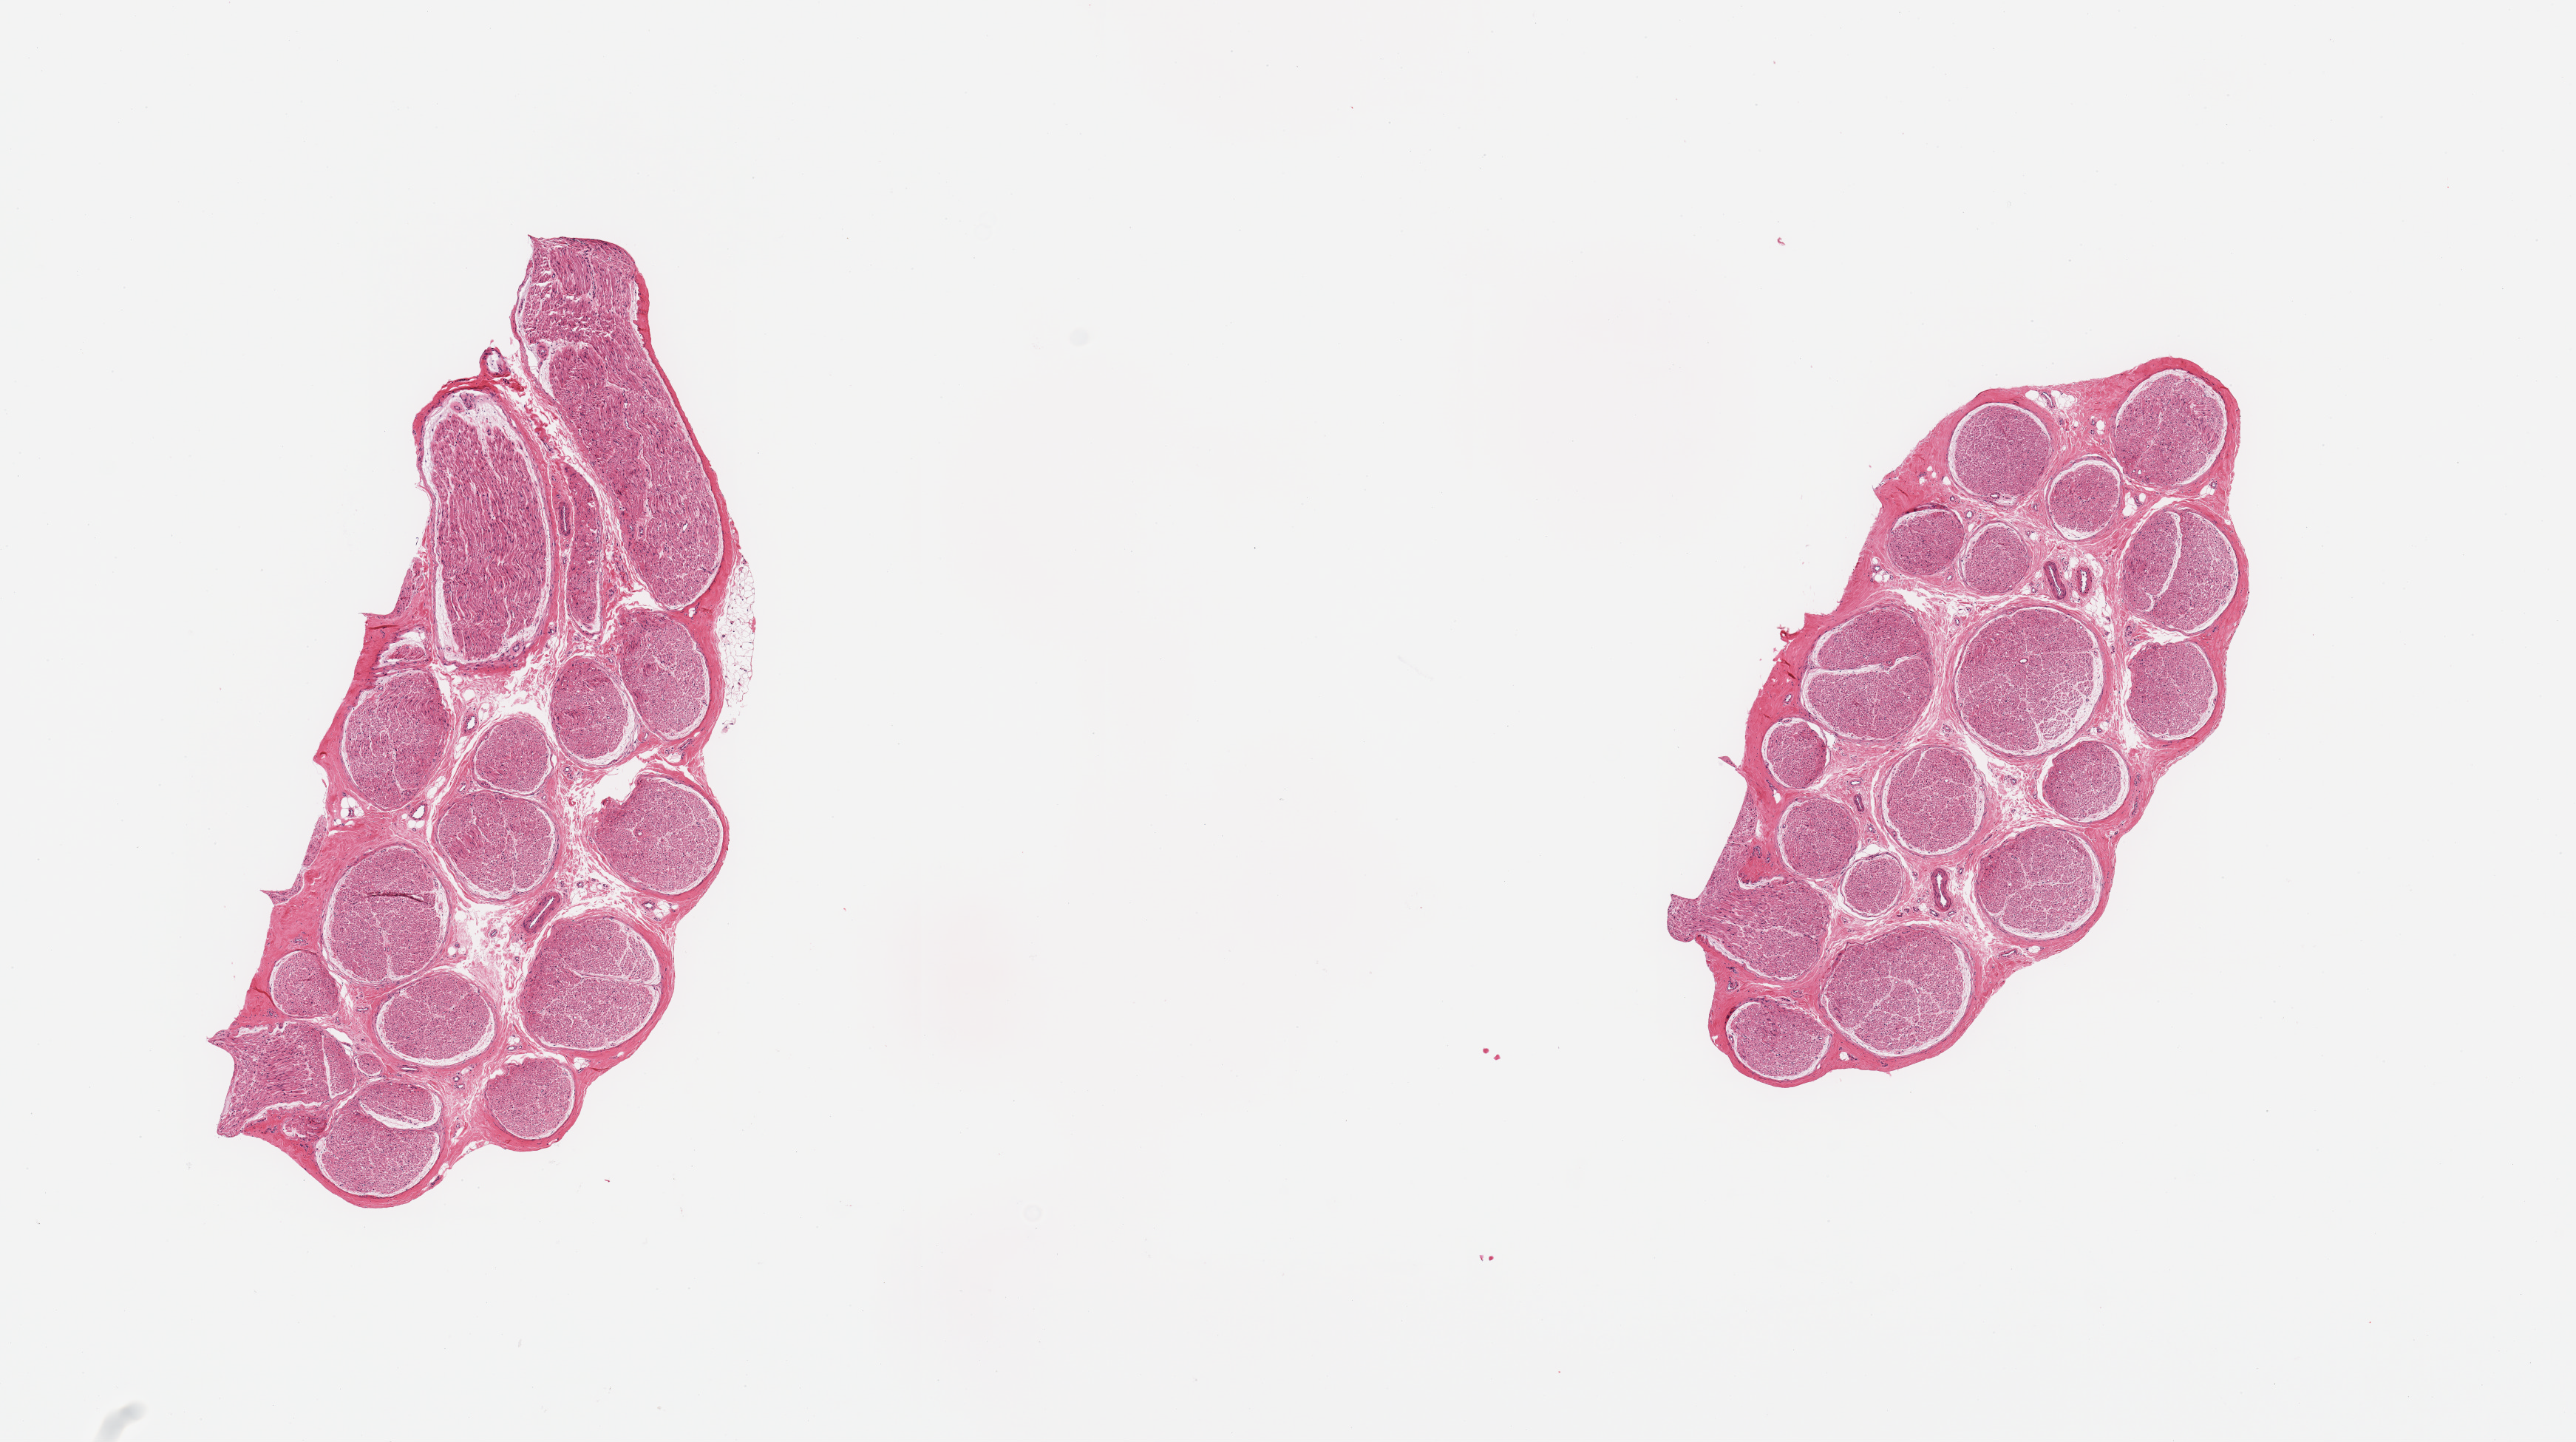
Haematoxylin and eosin whole-slide image, brightfield, low-resolution overview of the scanned area, about 13.8 x 7.7 mm. PAXgene-fixed paraffin-embedded (PFPE) section. Target tissue: tibial nerve. Tissue donor sample.
Reviewer comment on this tissue sample: 2 pieces; well trimmed.